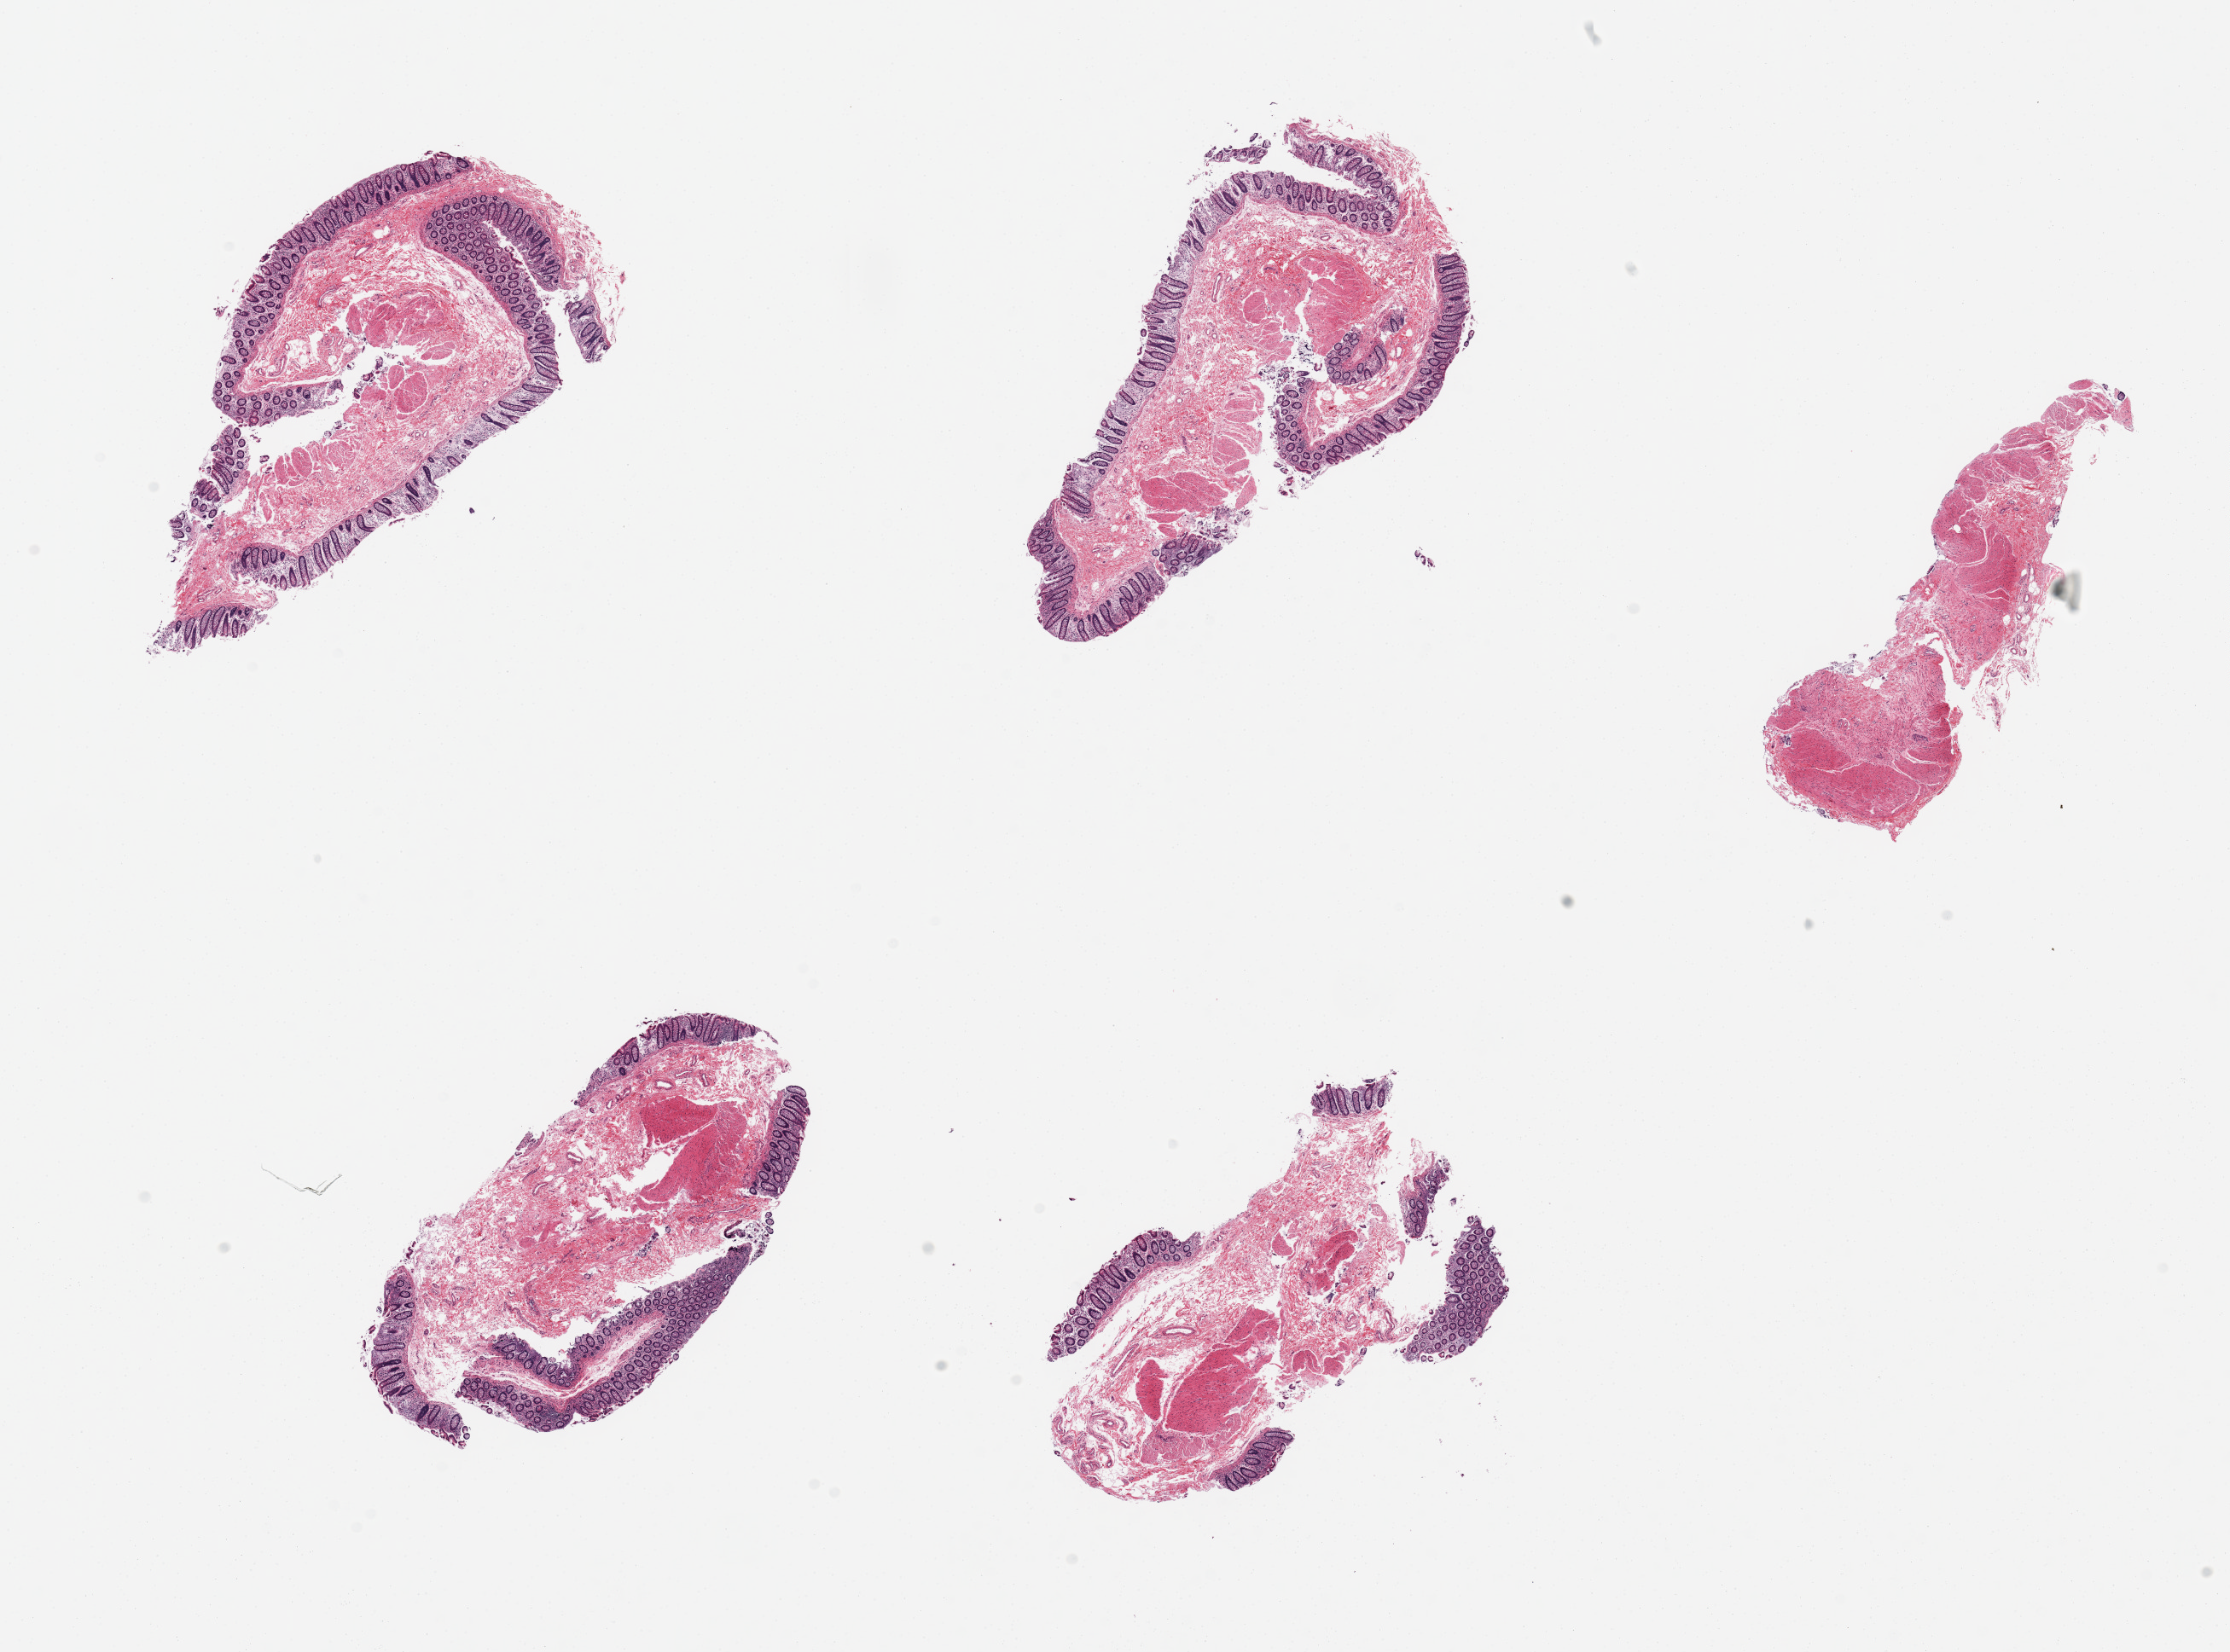
Haematoxylin and eosin whole-slide image, shown as a low-resolution overview of the whole scanned area (about 20.7 x 15.3 mm); PAXgene-fixed paraffin-embedded (PFPE) section; target tissue: sigmoid colon; tissue donor sample.
Reviewer comment on this tissue sample: 5 pieces; 4 pieces are full thickness with abundant mucosa; muscularis is target.